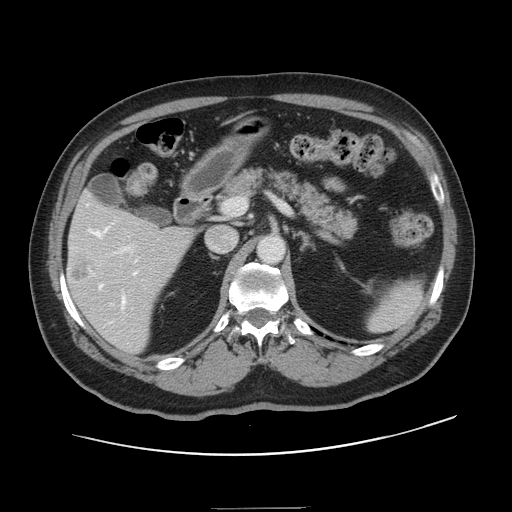
Contrast-enhanced abdominal CT, one axial slice. Position 78 of 143 along the scan axis. Intravenous contrast given. Soft-tissue window (W 400 / L 40 HU). 2.5 mm slice thickness. 512 × 512 image matrix, field of view 402 × 402 mm. Male patient, age 62 years. Case-level facts recorded for this patient, not image findings: diagnosis: colorectal cancer liver metastases, imaged before liver resection.
Outlined on this slice (expert manual segmentation):
- hepatic veins: bounding box <87,204,137,309> (left, top, right, bottom; pixels)
- liver: <67,195,191,352>
- planned liver remnant (the part of the liver to remain after resection): <73,196,136,229>
- portal vein (with intrahepatic branches): <110,247,132,323>
- liver metastasis: <73,263,90,283>